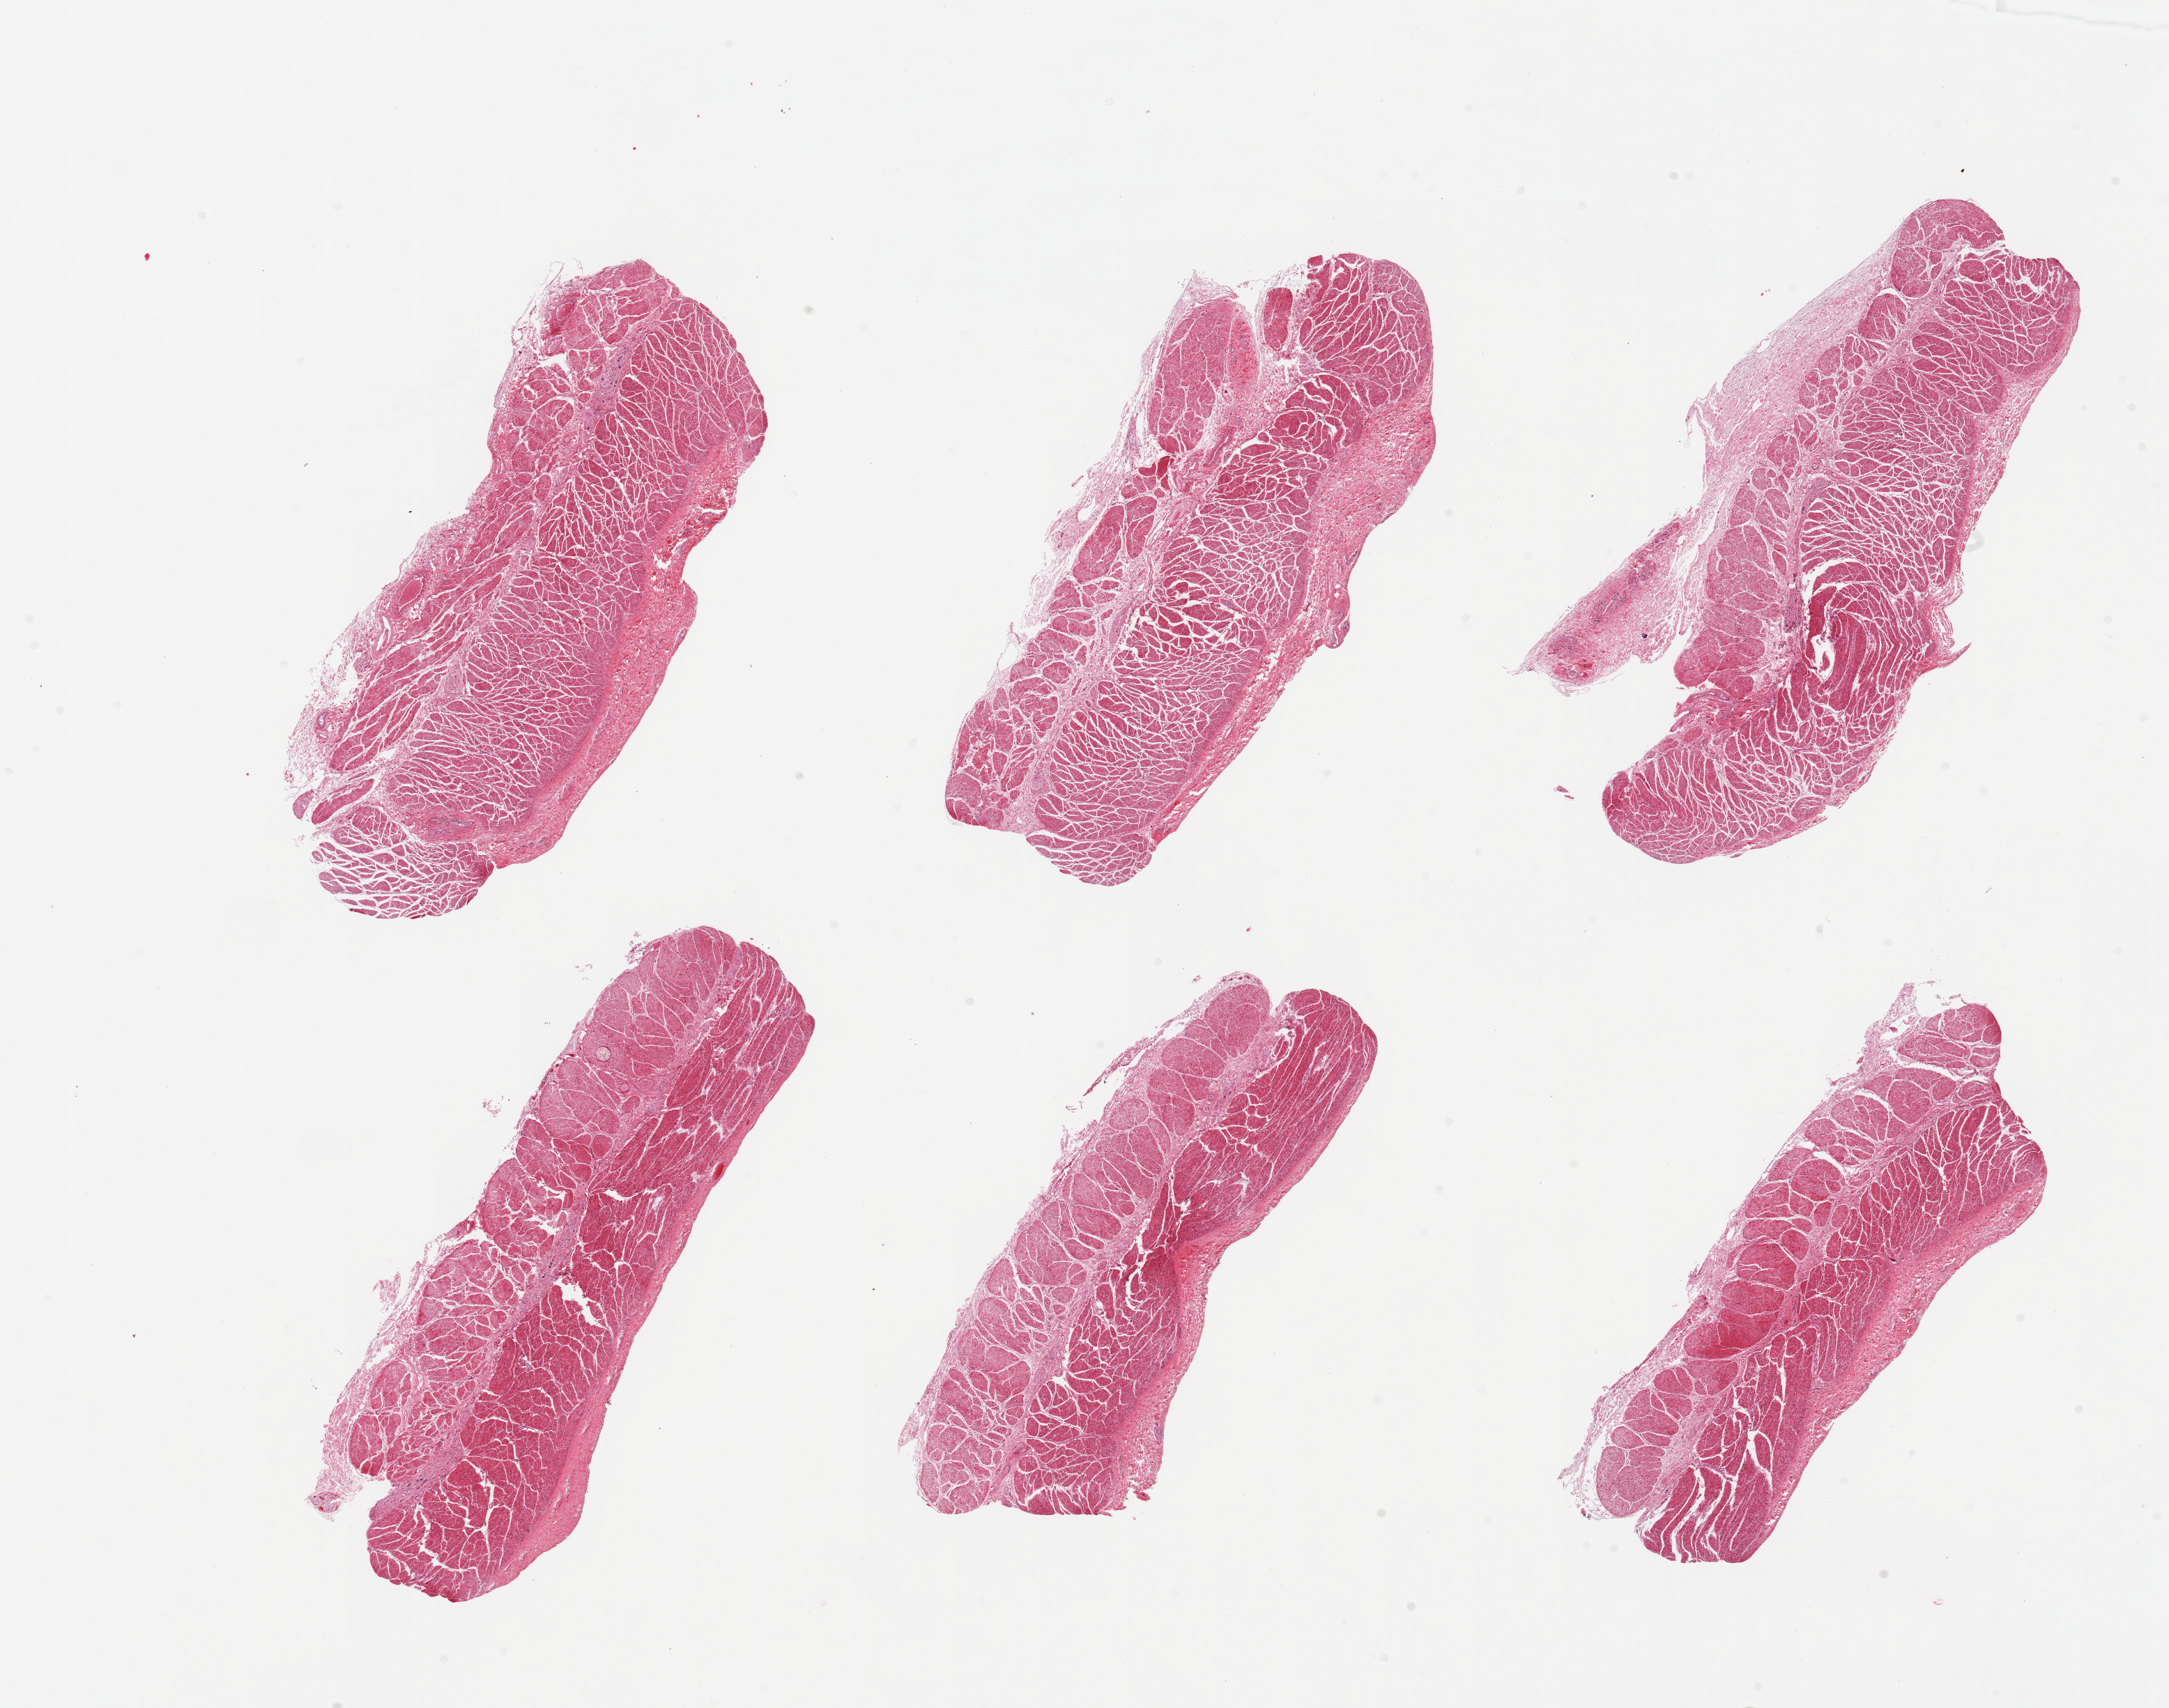
Whole-slide image, H&E stain, brightfield — low-resolution overview of the scanned area, about 24.6 x 19.4 mm; PAXgene-fixed paraffin-embedded (PFPE) section; section of gastroesophageal junction (target tissue); donor tissue sample. Donor: female.
Review note (as recorded): 6 pieces, confirmed targemt muscularis.